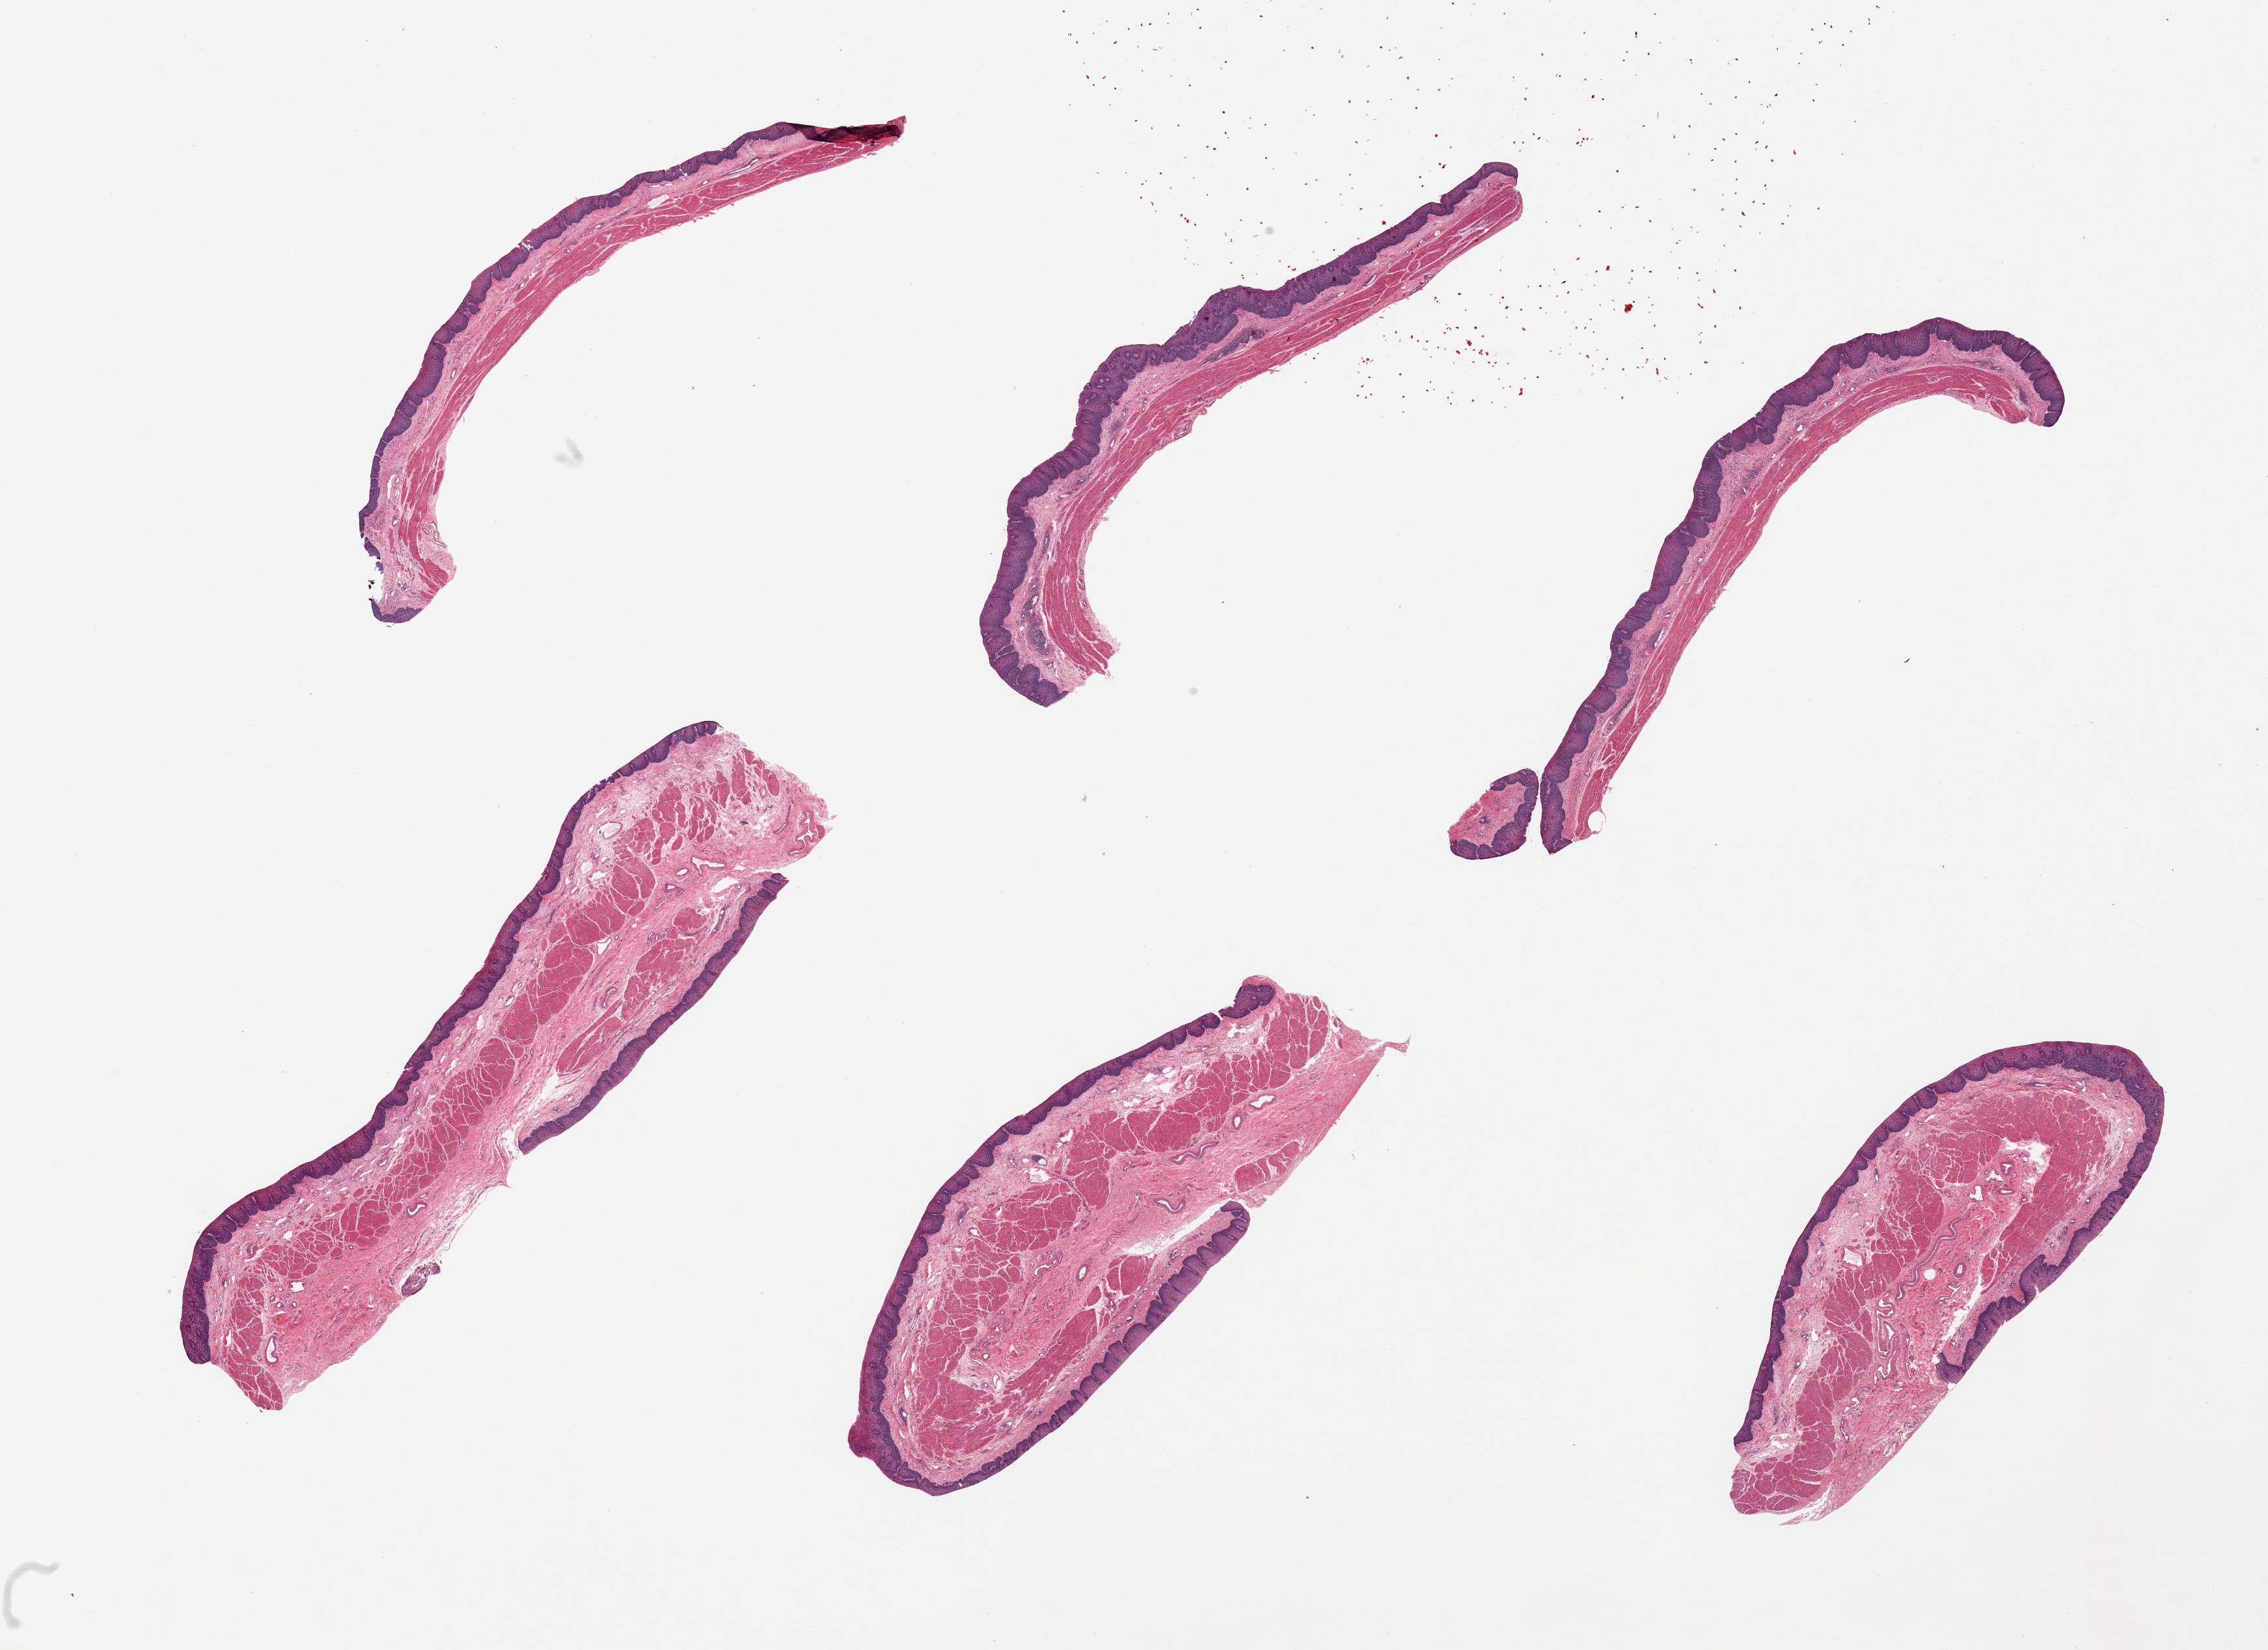
Haematoxylin and eosin whole-slide image — shown as a low-resolution overview of the whole scanned area (about 27.6 x 20.1 mm). PAXgene-fixed, paraffin-embedded tissue. Section of esophageal mucous membrane (target tissue). Tissue donor sample. Female donor.
Reviewer comment on this tissue sample: 6 pieces, squamous mucosa is 0.25-0.5mm thick.